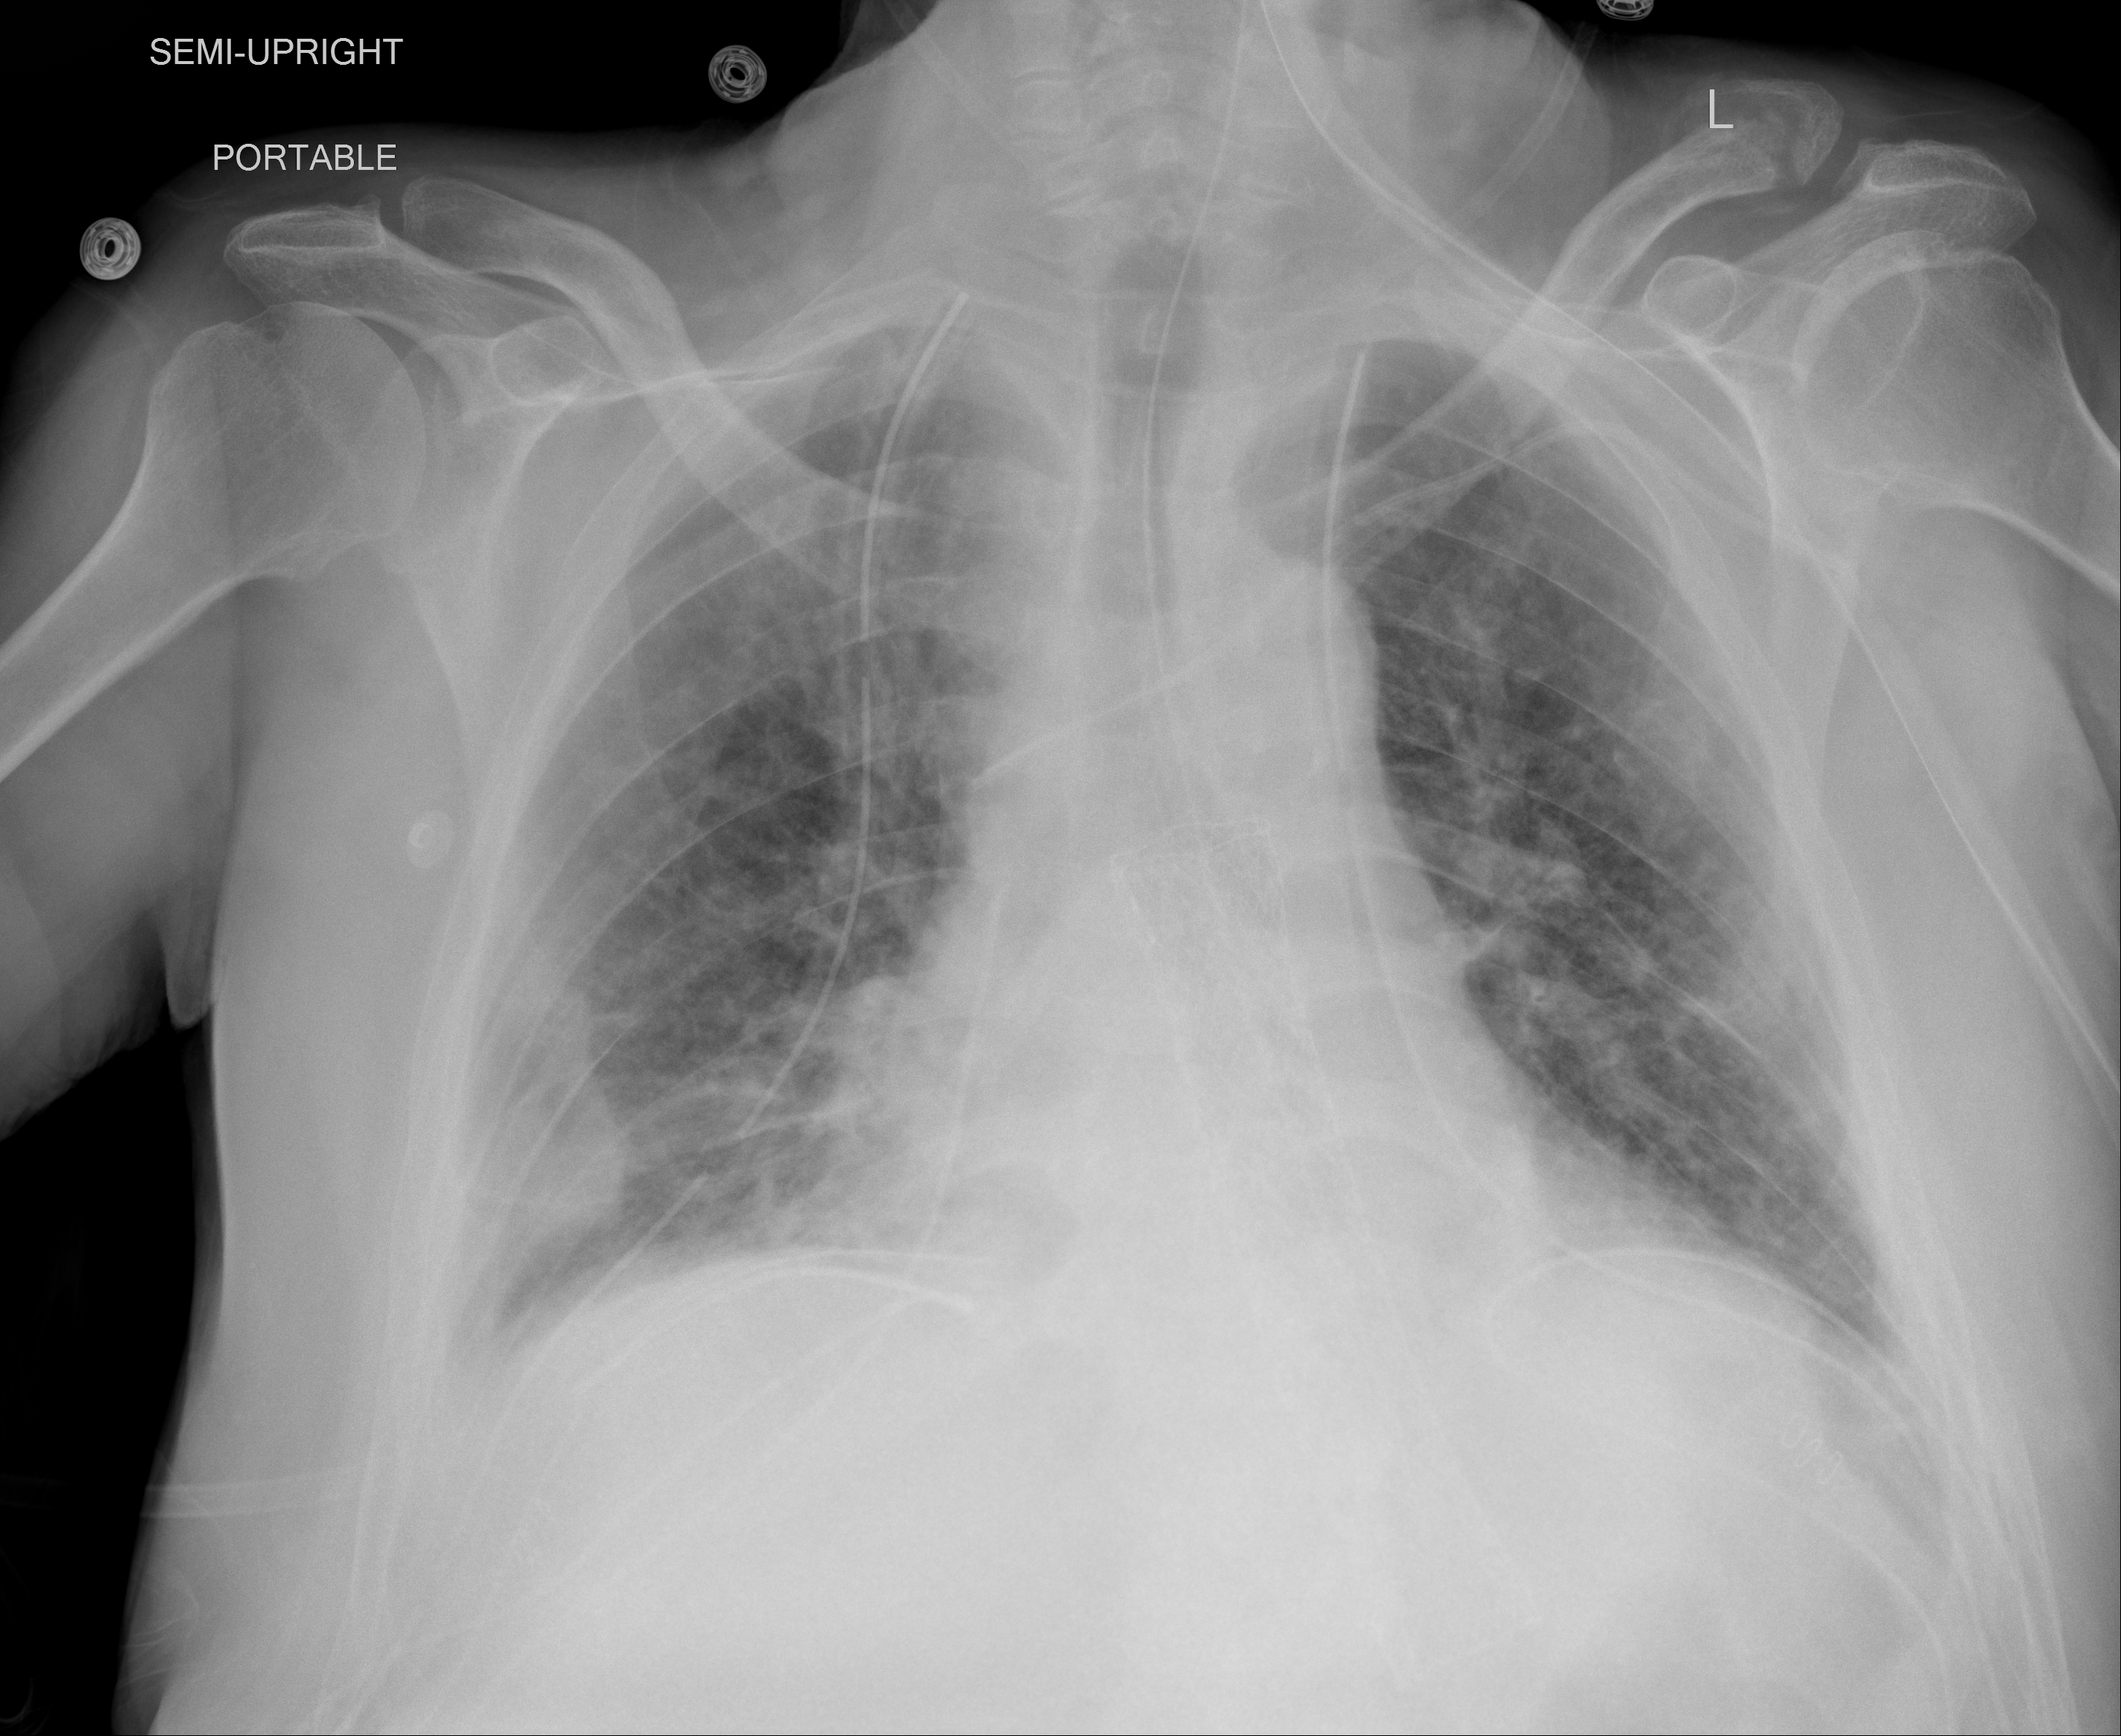
Chest X-ray (portable), AP projection. Male patient, age 64 years; imaged 4 days after the COVID-19 diagnosis.
Radiologist's key findings for this exam: Patchy bibasilar opacities again seen likely atelectasis, no change.